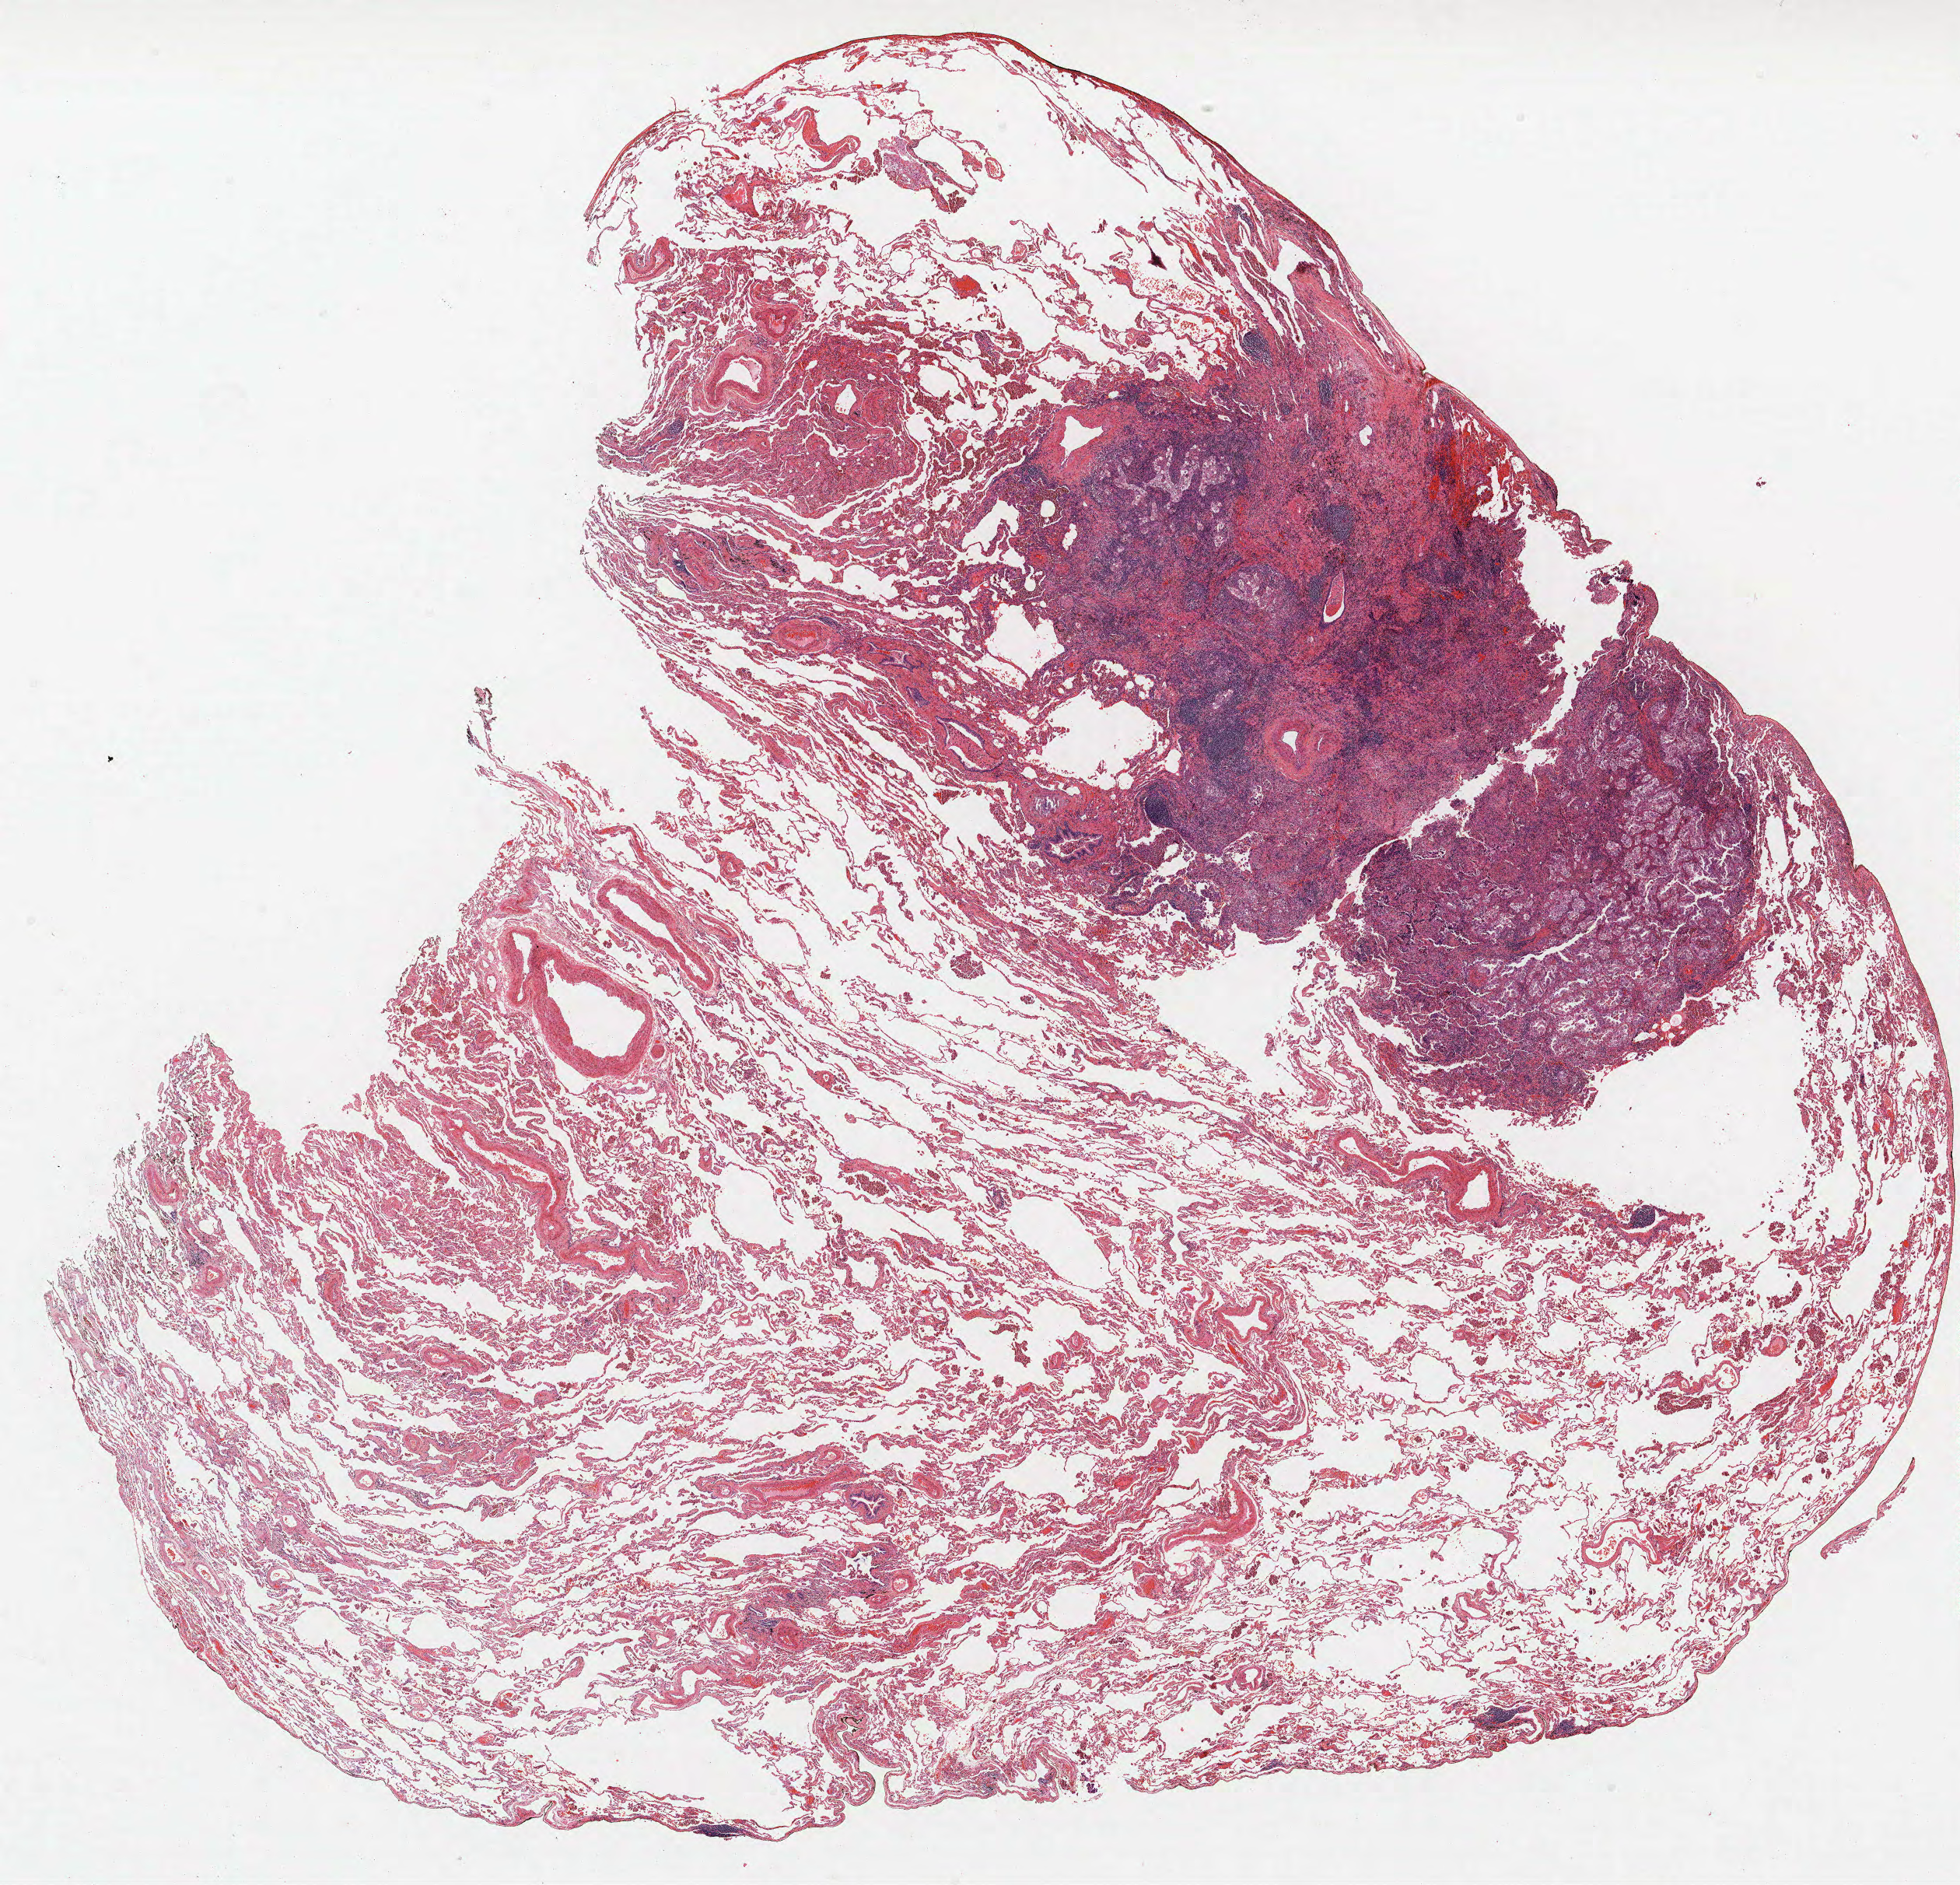
H&E whole-slide image — shown as a low-resolution overview of the whole scanned area (about 20.2 x 19.4 mm), FFPE section, lung. Female patient, aged 67 at enrolment.
Participant's lung-cancer diagnosis: Adenocarcinoma, NOS.